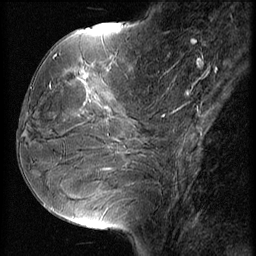
Breast MRI (dynamic contrast-enhanced), one sagittal slice. Slice 22 of 56 in the series (ordered by position). 3 images stored at this slice position (order not interpretable as contrast timing). 1.5 T. TE 4.2 ms, TR 9 ms. 2.5 mm slice thickness. 256 × 256 image matrix. Female patient, age 51 years. From the clinical record (not read from this slice): setting: breast cancer imaged before/during neoadjuvant chemotherapy; receptor status: HR-positive, HER2-negative.
Outlined on this slice (semi-automatically segmented with operator editing):
- analysis volume of interest (the breast-tissue region the enhancement analysis was run in; not a lesion): box from (x=23, y=56) to (x=156, y=165) px
- tumour enhancement mask (voxels above the 140 % enhancement threshold inside the analysis volume of interest): (x=76, y=62)–(x=117, y=119)